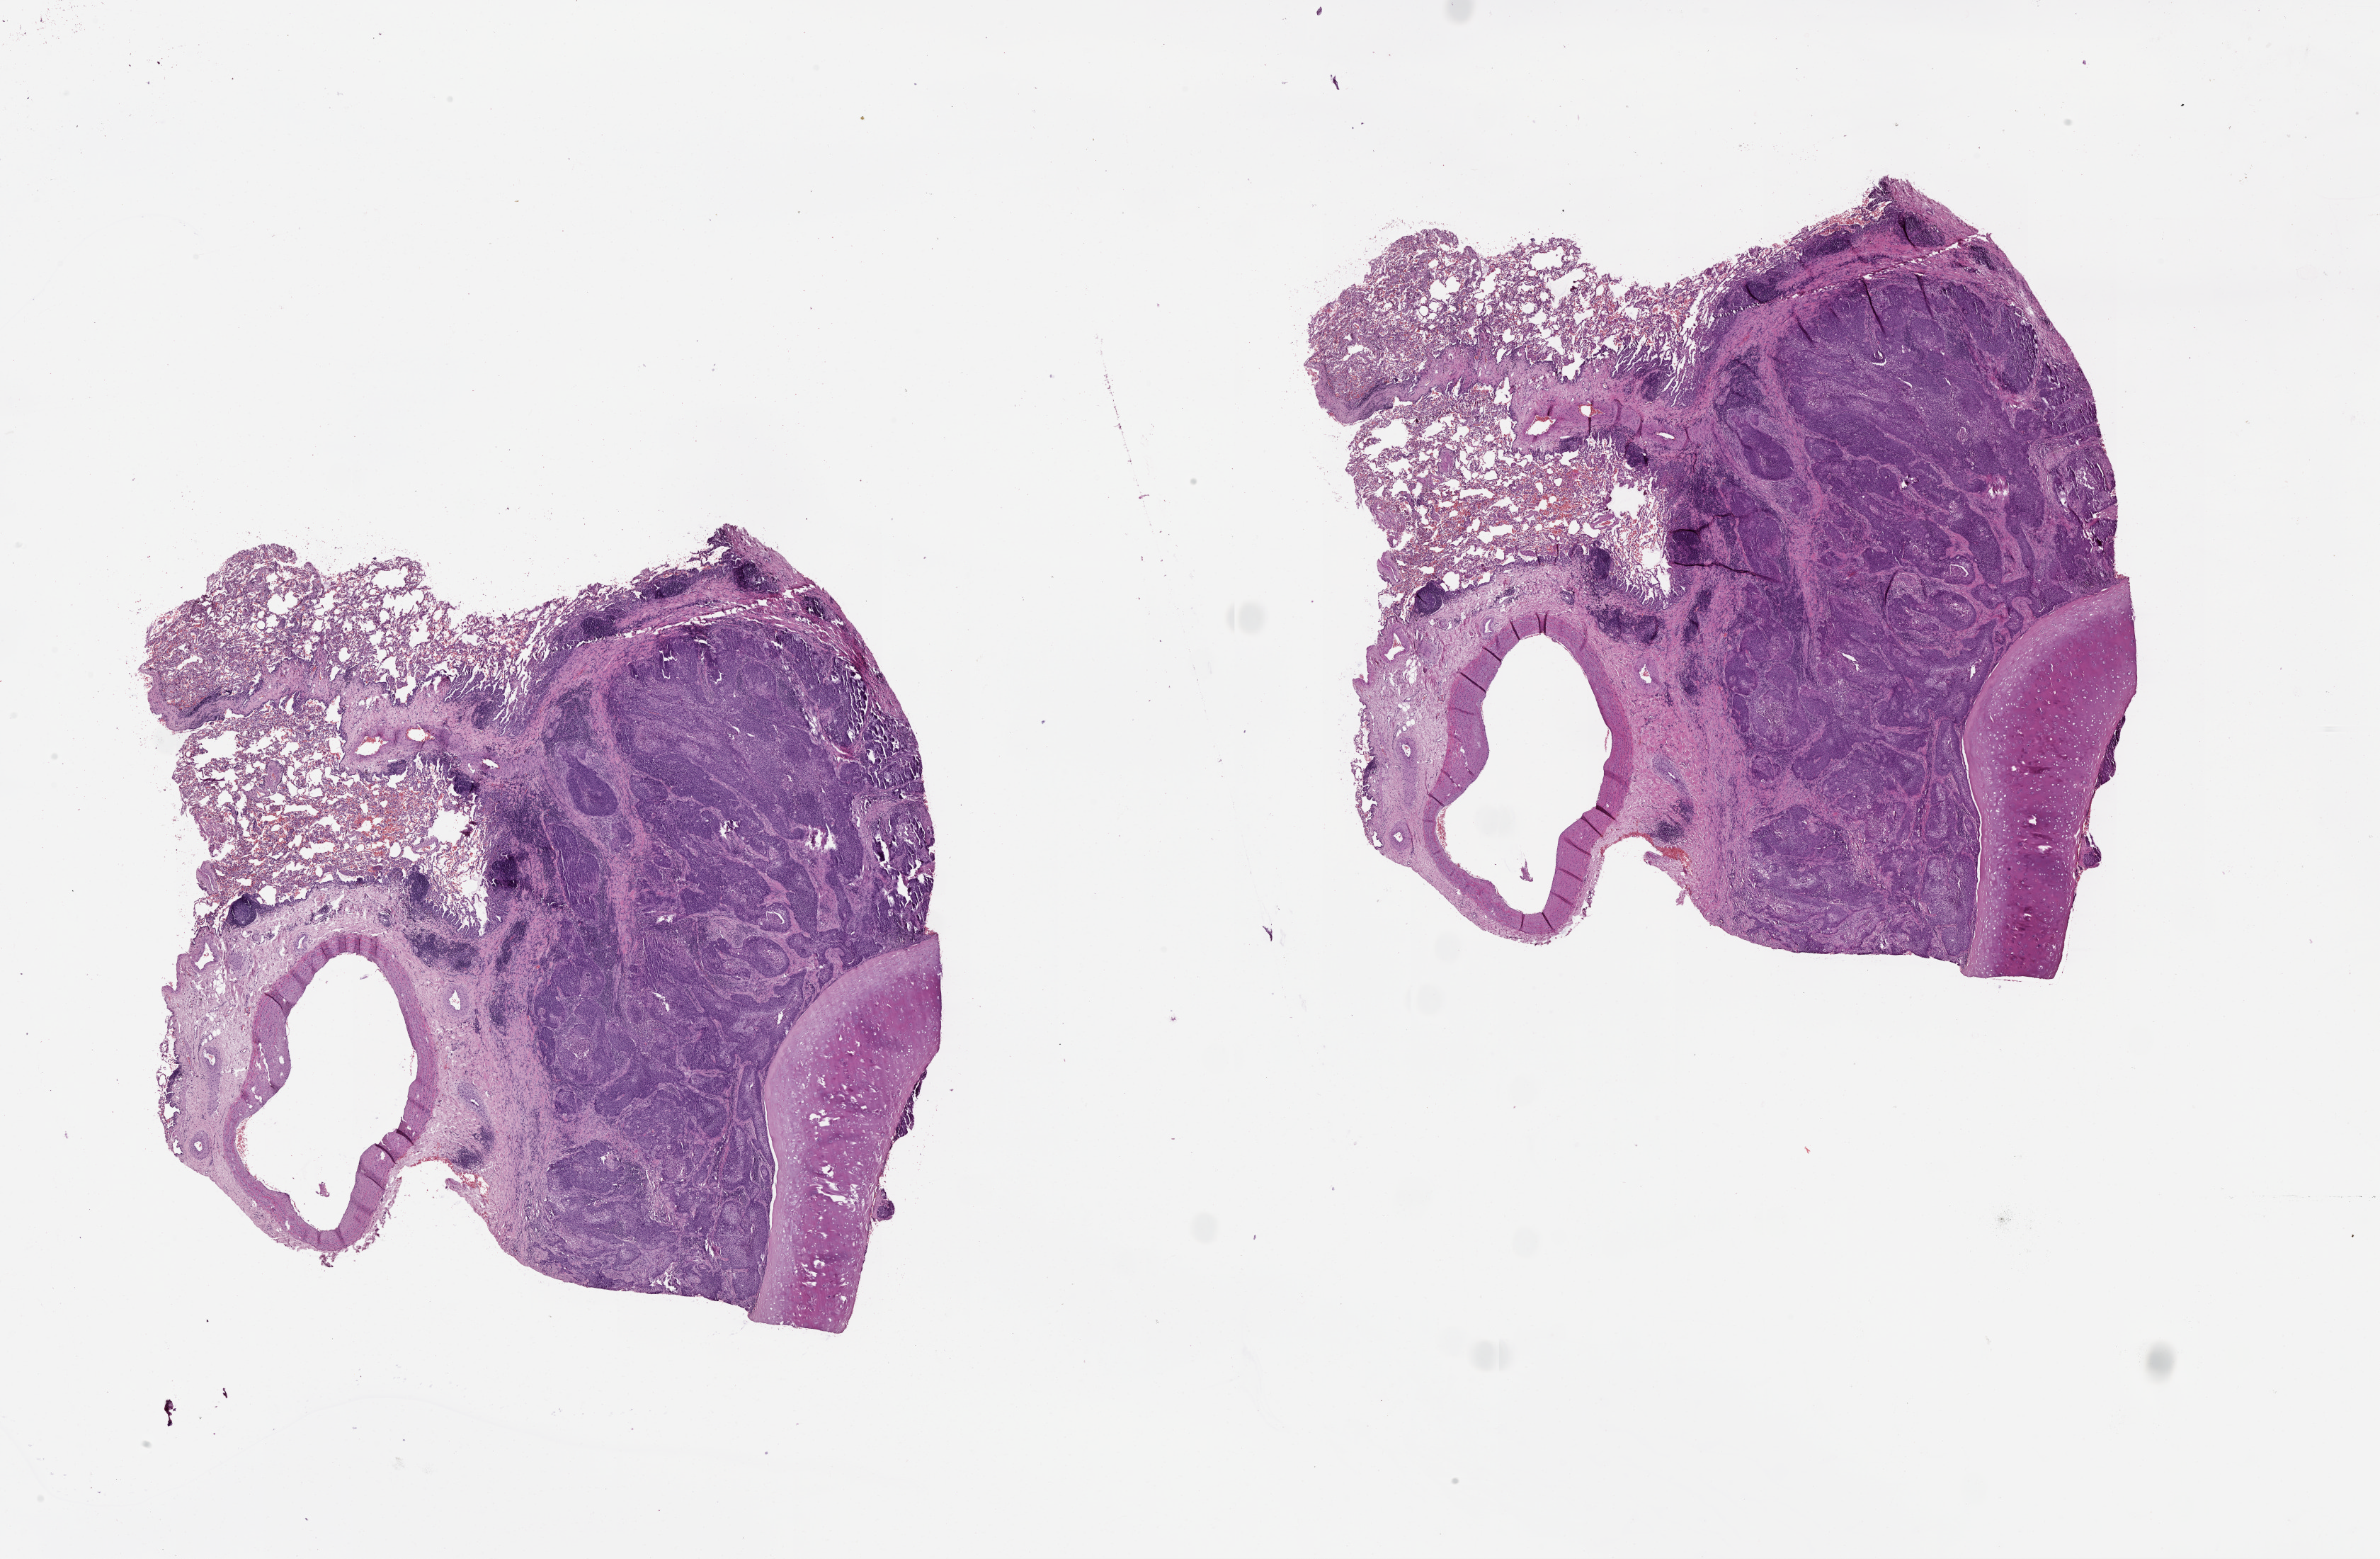
Digitized Hematoxylin and eosin (H&E) stained tissue section (whole slide), shown as a low-resolution overview of the whole scanned area (about 27.1 x 17.7 mm, acquisition: 20x scan). Lung, tumour tissue. Male, 53 y/o.
* patient diagnosis (cohort enrolment): squamous cell carcinoma (lung)